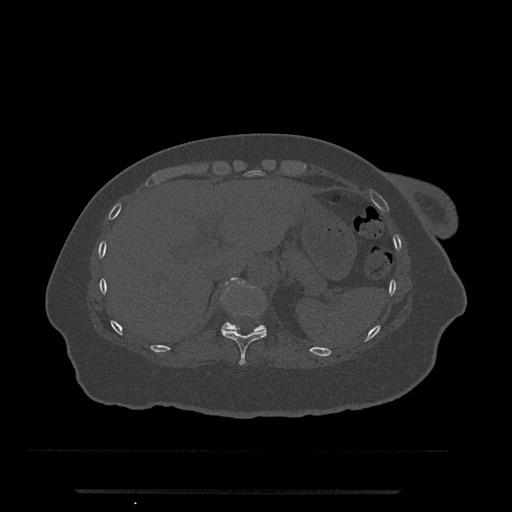
CT including the spine, one axial slice; position 267 of 797 along the scan axis; reconstruction kernel Br40s/3; 120 kVp; bone window (W 1800 / L 400 HU); 512 × 512 image matrix, field of view 440 × 440 mm. Female patient, age 51 years. From the clinical record (not read from this slice): primary cancer: neuro.
Annotated regions visible in this slice (semi-automatic segmentation, software-assisted and operator-edited):
- T10 vertebra: bounding box [x1, y1, x2, y2] px = [221, 277, 267, 366]
- T11 vertebra: [222, 298, 264, 331]